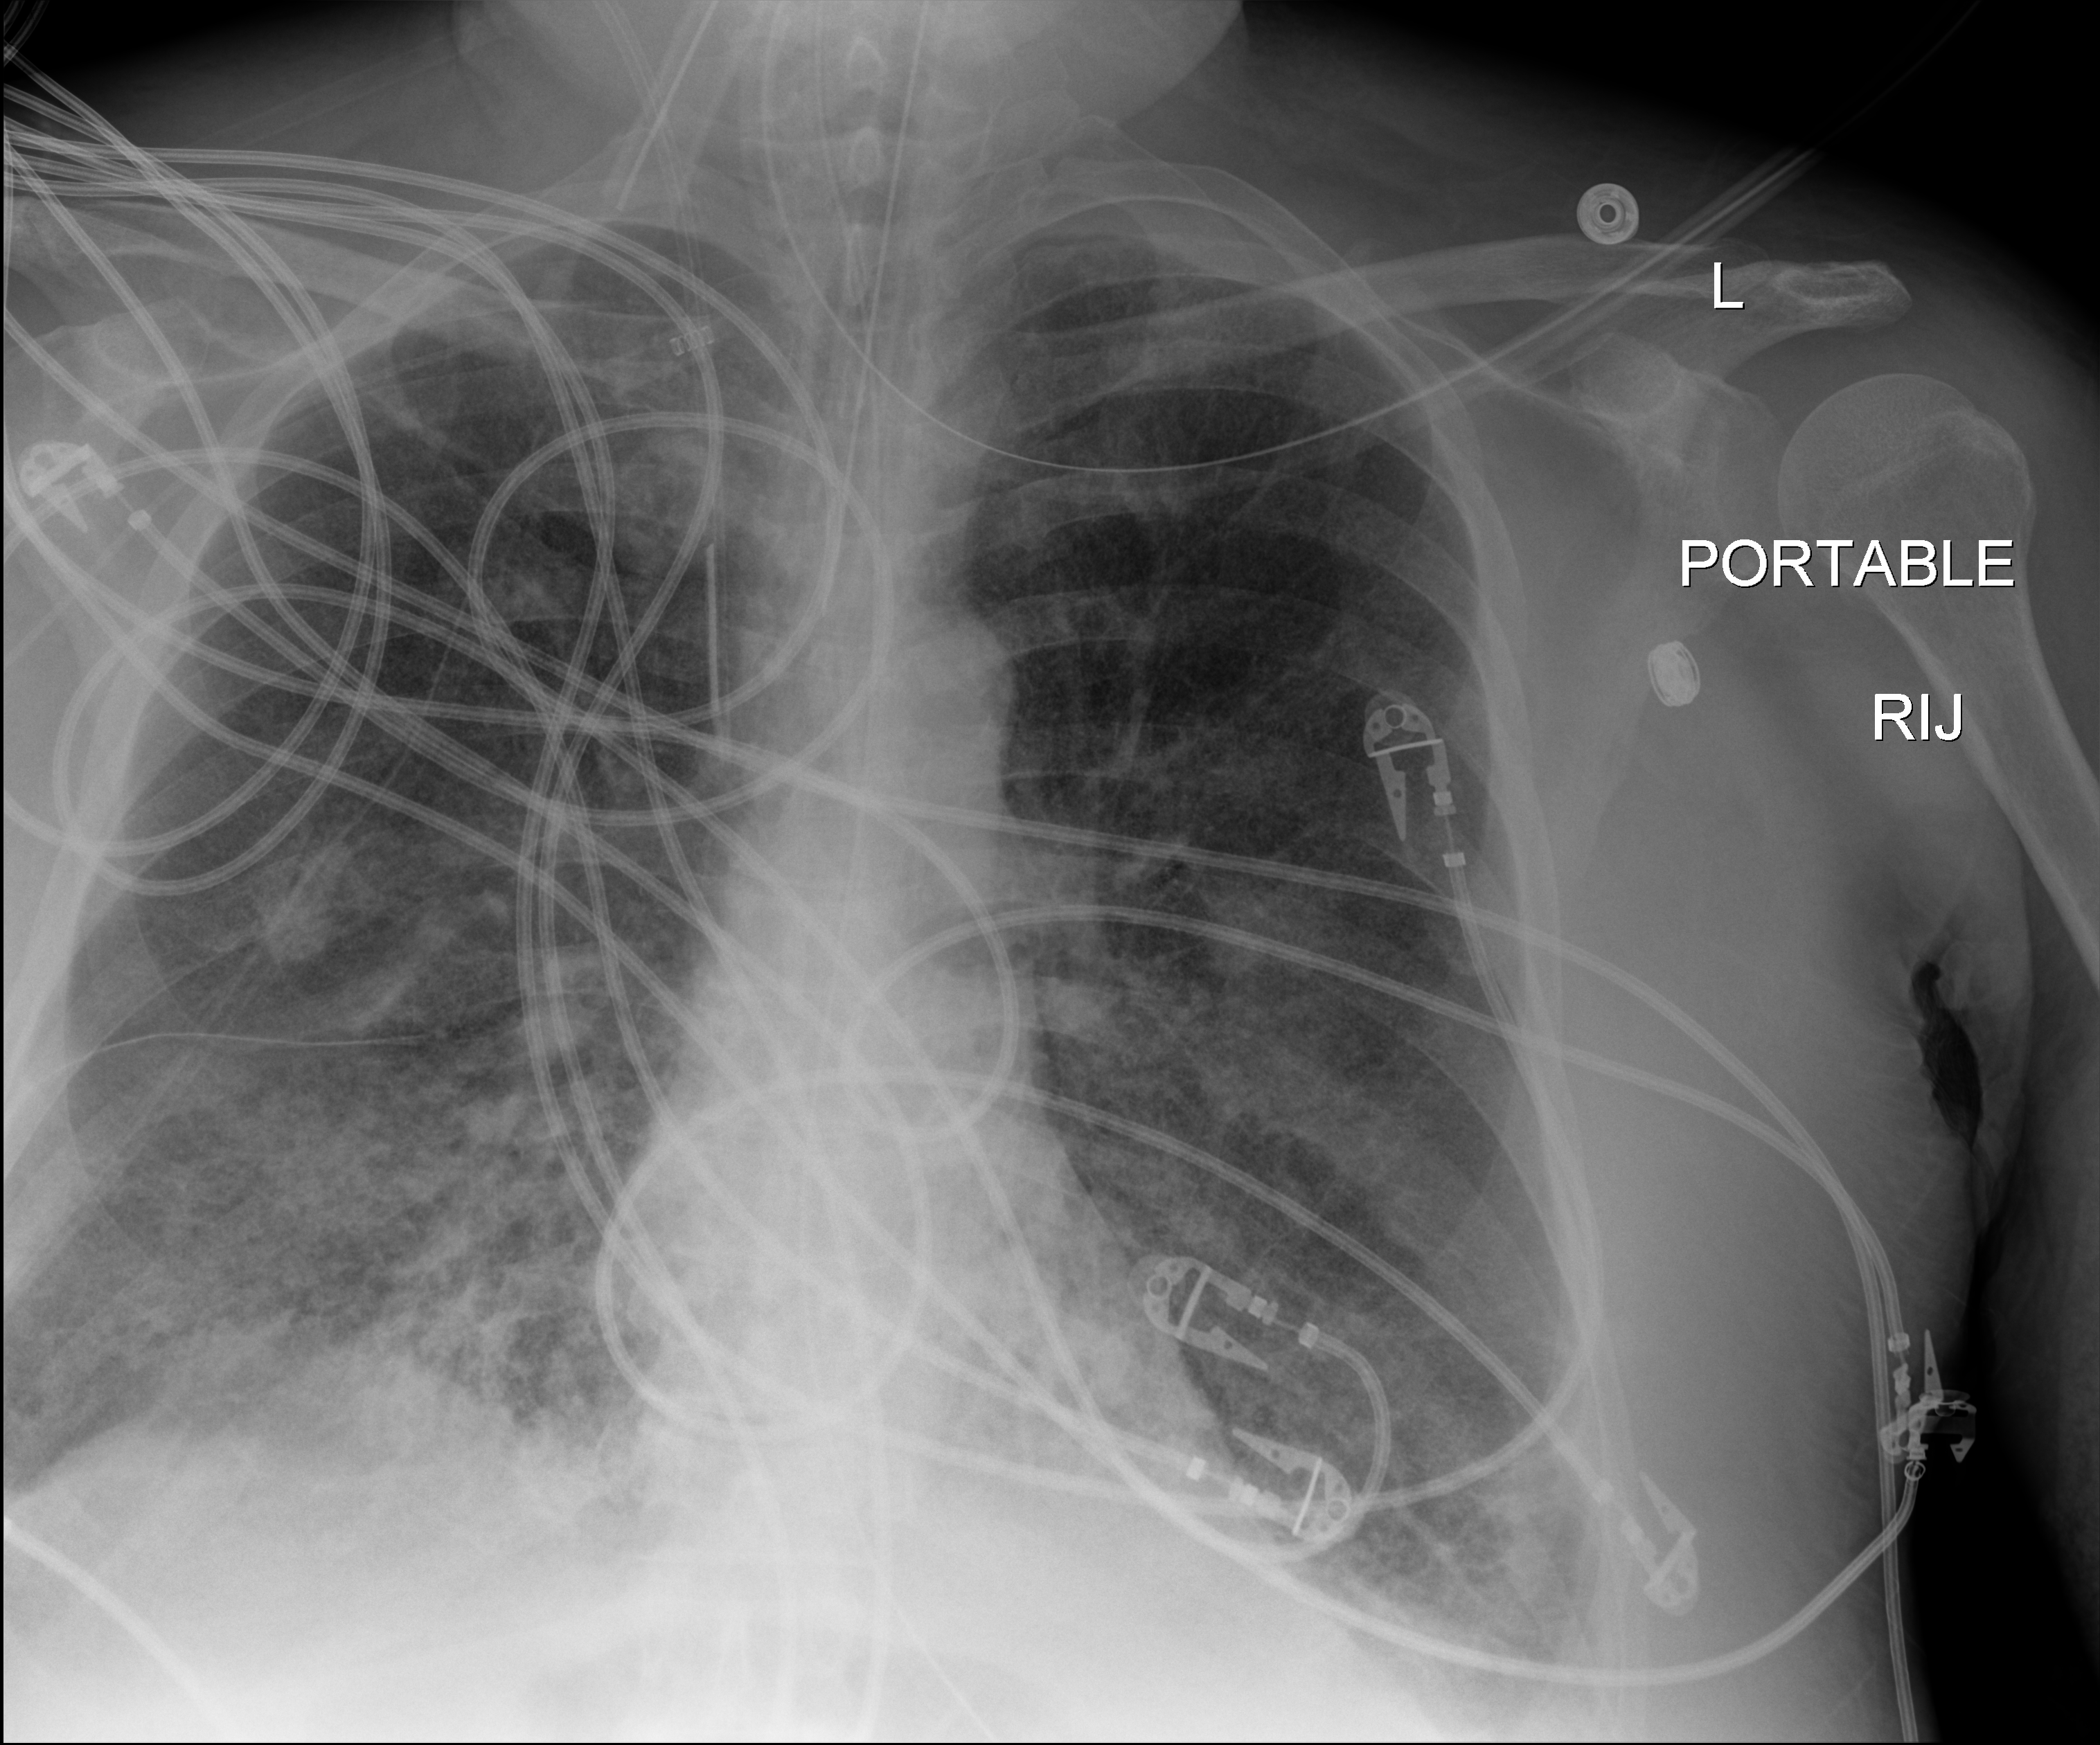
Portable chest radiograph. Patient hospitalised with COVID-19; male, aged 60–74 years.
Admission-level facts for this patient (not findings on this image; timing relative to this image not recorded):
- chronic kidney disease (admission record): no
- hypertension (admission record): no
- smoking status (admission record): former